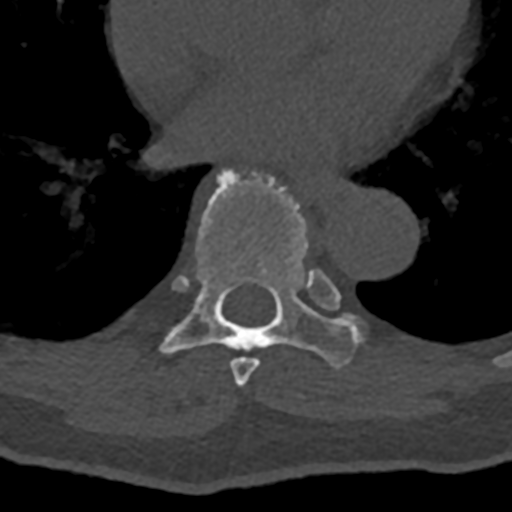
CT including the spine, one axial slice; slice 719 of 797 in the series (ordered by position); bone window (W 1800 / L 400 HU); 512 × 512 image matrix, field of view 160 × 160 mm. Male patient, age 74 years. Case-level facts recorded for this patient, not image findings: primary cancer: renal.
Annotated regions visible in this slice (semi-automatic segmentation, software-assisted and operator-edited):
- T7 vertebra: bounding box (x1, y1, x2, y2) in pixels: (230, 269, 337, 387)
- T8 vertebra: (161, 167, 362, 368)